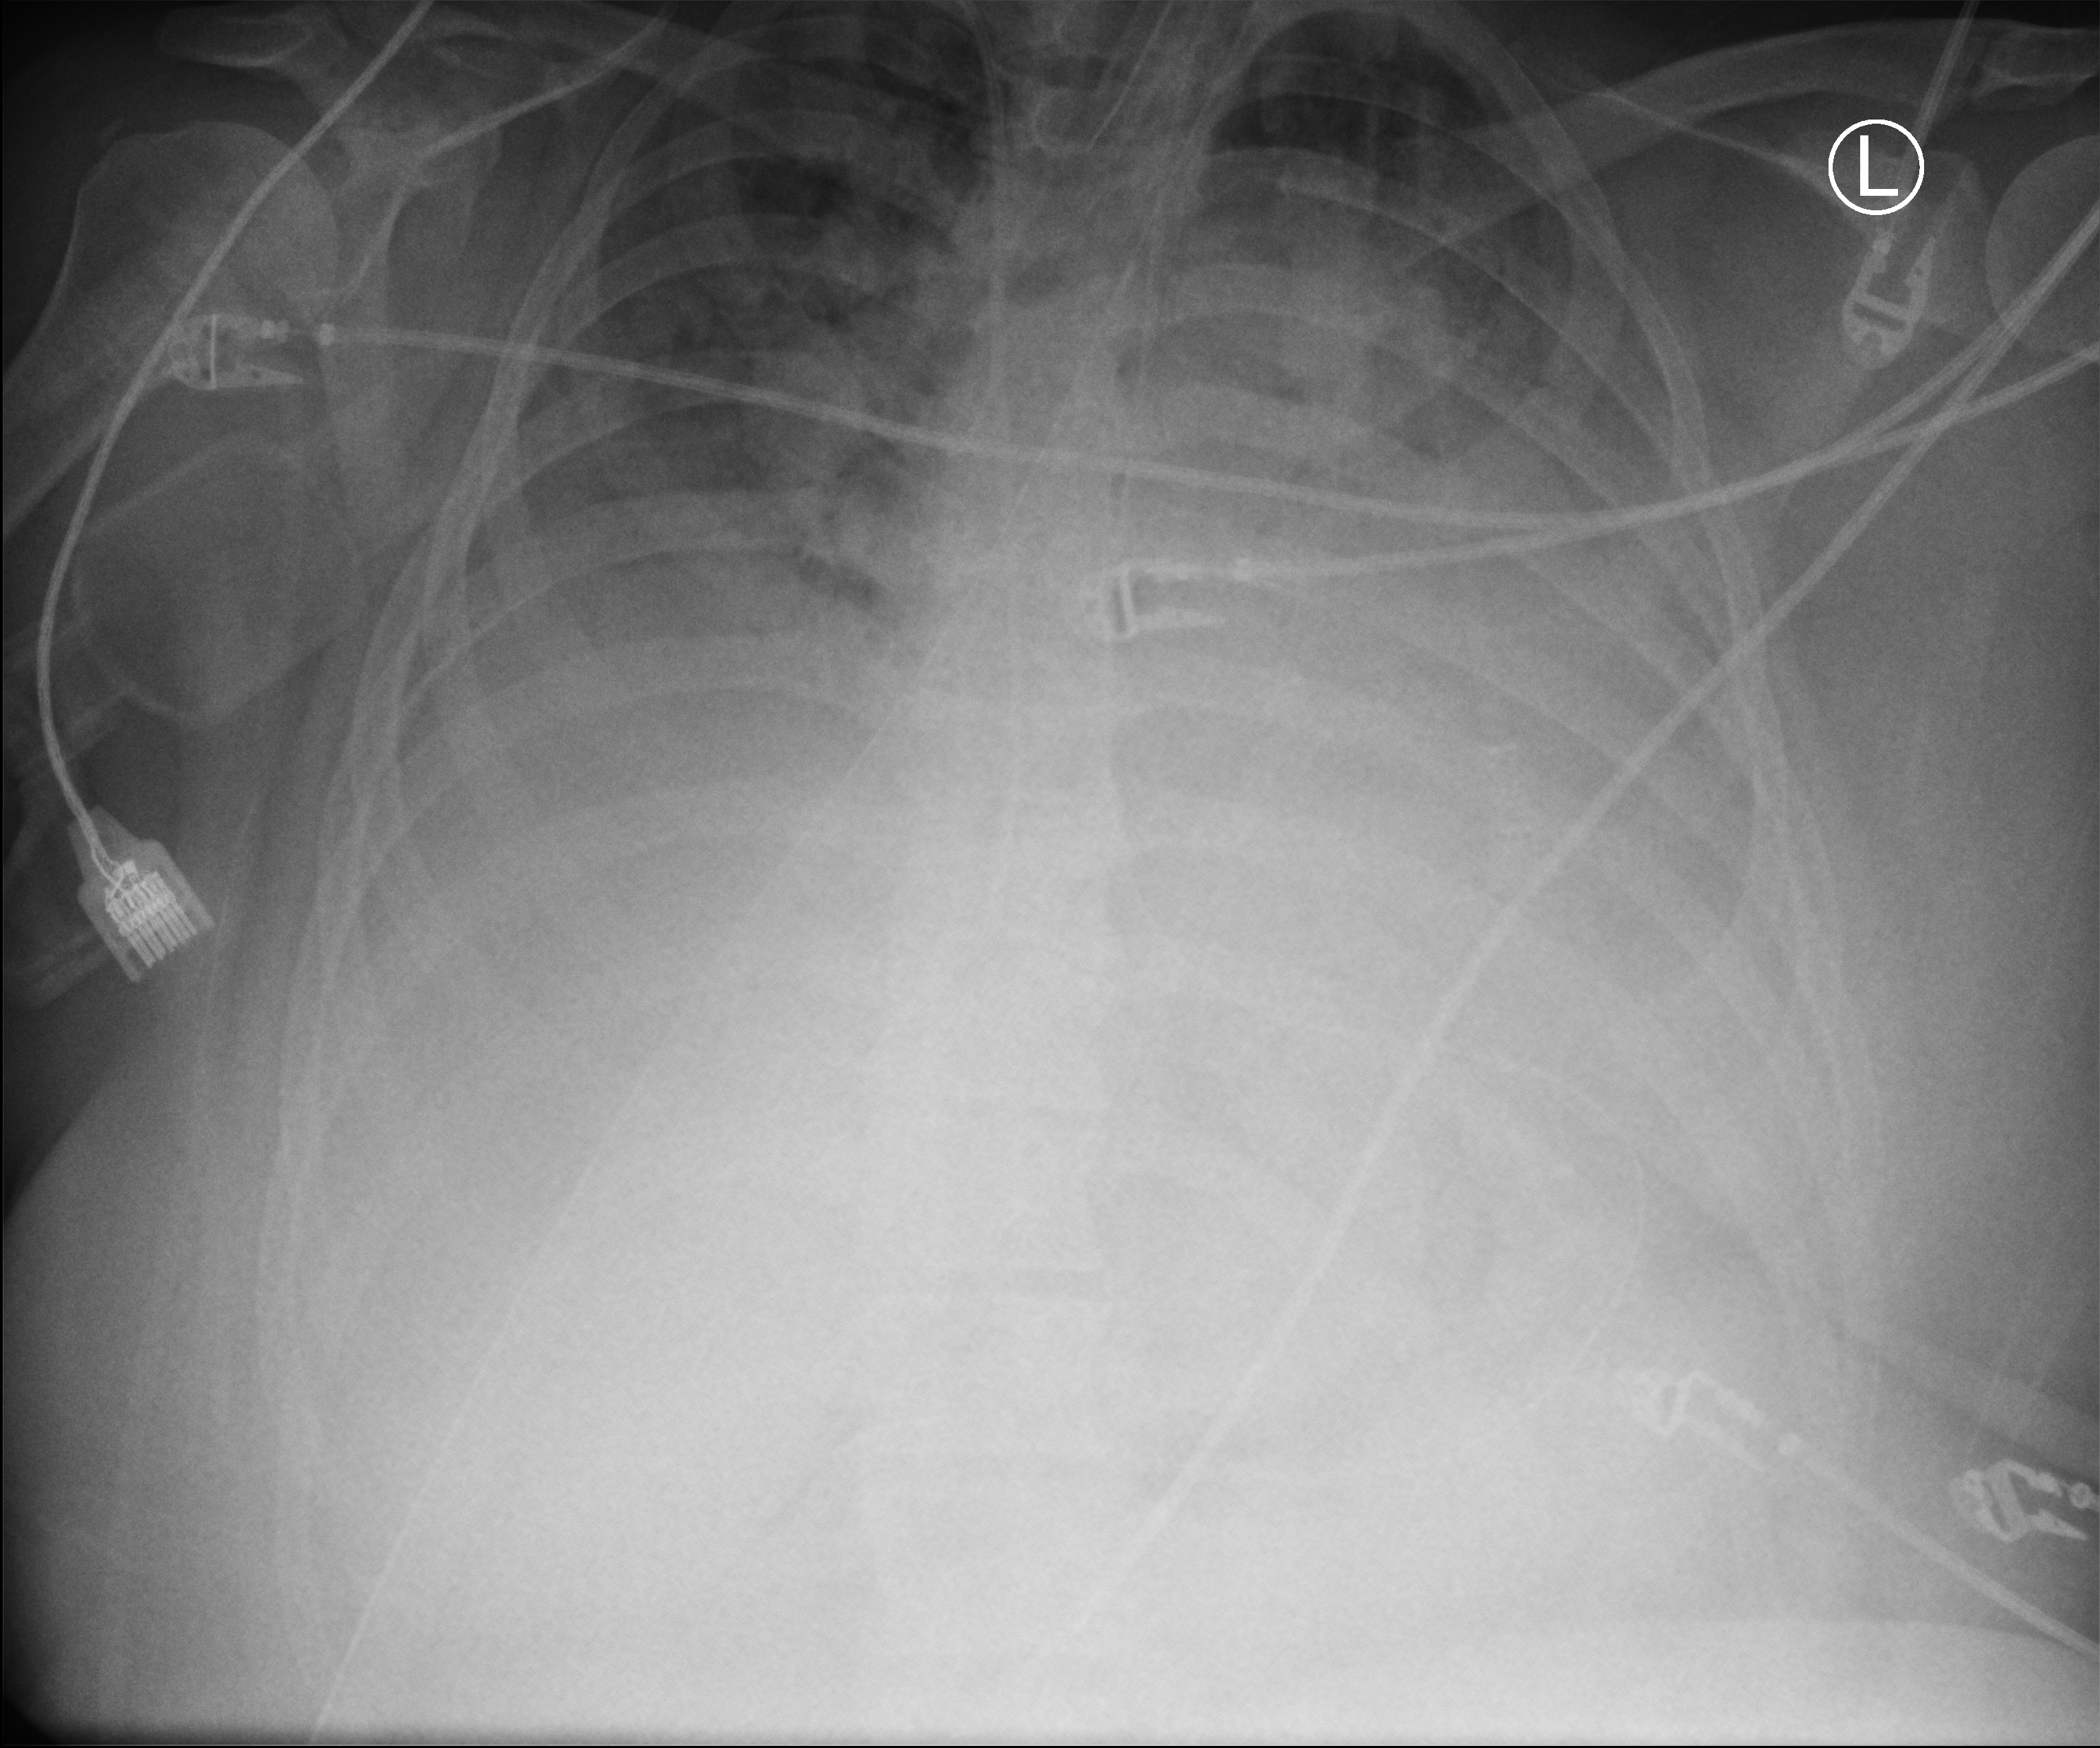
Bedside chest radiograph (computed radiography); anteroposterior (AP) projection. Female patient hospitalised with COVID-19, age 18–59 years.
From the hospital-stay record, not from the radiograph (when in the stay this image was taken is not recorded): chronic kidney disease (admission record): no; hypertension (admission record): no; mechanically ventilated during this hospital stay: yes.